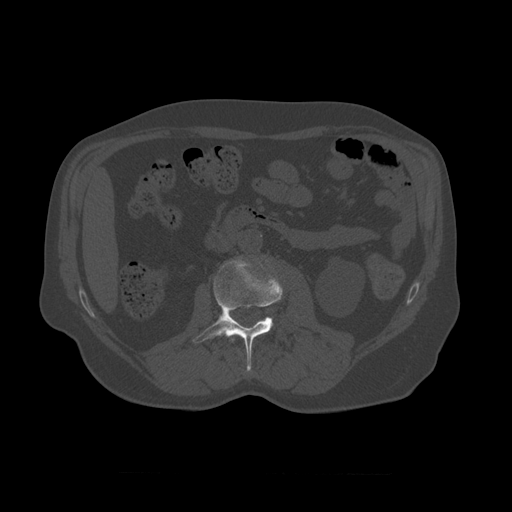
CT including the spine, one axial slice. Slice 327 of 450 in the series (ordered by position). Reconstruction kernel STANDARD. Bone window (W 1800 / L 400 HU). 1.25 mm slice thickness. 512 × 512 image matrix, field of view 405 × 405 mm. Patient age 75 years. Case-level facts recorded for this patient, not image findings: primary cancer: prostate.
Annotated regions visible in this slice (semi-automatic segmentation, software-assisted and operator-edited):
- L1 vertebra: bounding box (x1, y1, x2, y2) in pixels: (230, 336, 234, 342)
- L2 vertebra: (193, 258, 284, 373)